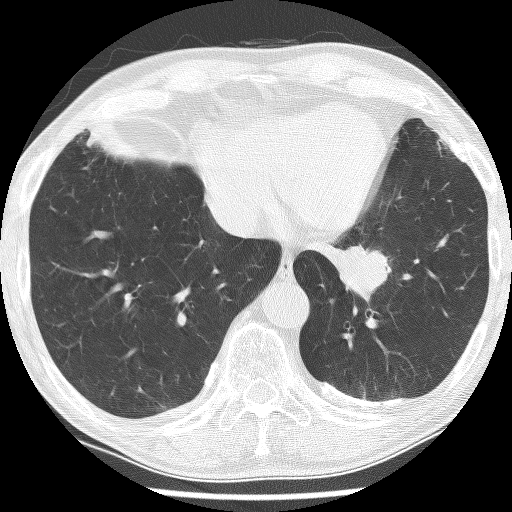
Low-dose screening chest CT, one axial slice. Slice 48 of 226 in the series (ordered by position). Reconstruction kernel BONE. 120 kVp. Lung window (W 1500 / L -600 HU). 512 × 512 image matrix, field of view 320 × 320 mm.
Outlined on this slice (expert manual segmentation):
- lesion 1 (tumor, lower lobe of left lung): bounding box (x1, y1, x2, y2) in pixels: (339, 246, 391, 298)